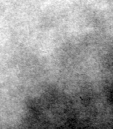
Crop from a digitized film mammogram around one marked abnormality, left breast, CC view.
Marked abnormality: calcifications, morphology amorphous / round and regular, distribution clustered; BI-RADS assessment category 4; subtlety rating 4 on a 1 (subtle) to 5 (obvious) scale; pathology result (as recorded, not read from the image): malignant.